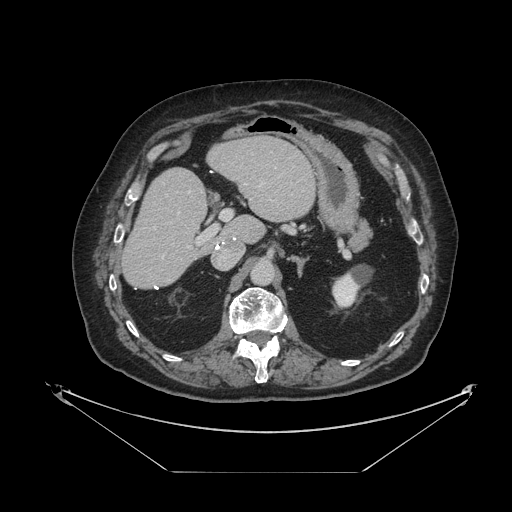
Contrast-enhanced abdominal CT, one axial slice. Slice 58 of 121 in the series (ordered by position). Reconstruction kernel STANDARD. Intravenous contrast given. Soft-tissue window (W 400 / L 40 HU). 2.5 mm slice thickness. 512 × 512 image matrix, field of view 500 × 500 mm. Male patient, age 68 years. Case-level facts recorded for this patient, not image findings: diagnosis: colorectal cancer liver metastases, imaged before liver resection; multiple liver metastases: no.
Structures marked on this image (outlined manually by an expert reader):
- hepatic veins: bounding box [x1, y1, x2, y2] px = [162, 183, 246, 259]
- liver: [122, 137, 316, 288]
- planned liver remnant (the part of the liver to remain after resection): [123, 137, 316, 288]
- portal vein (with intrahepatic branches): [187, 210, 232, 248]